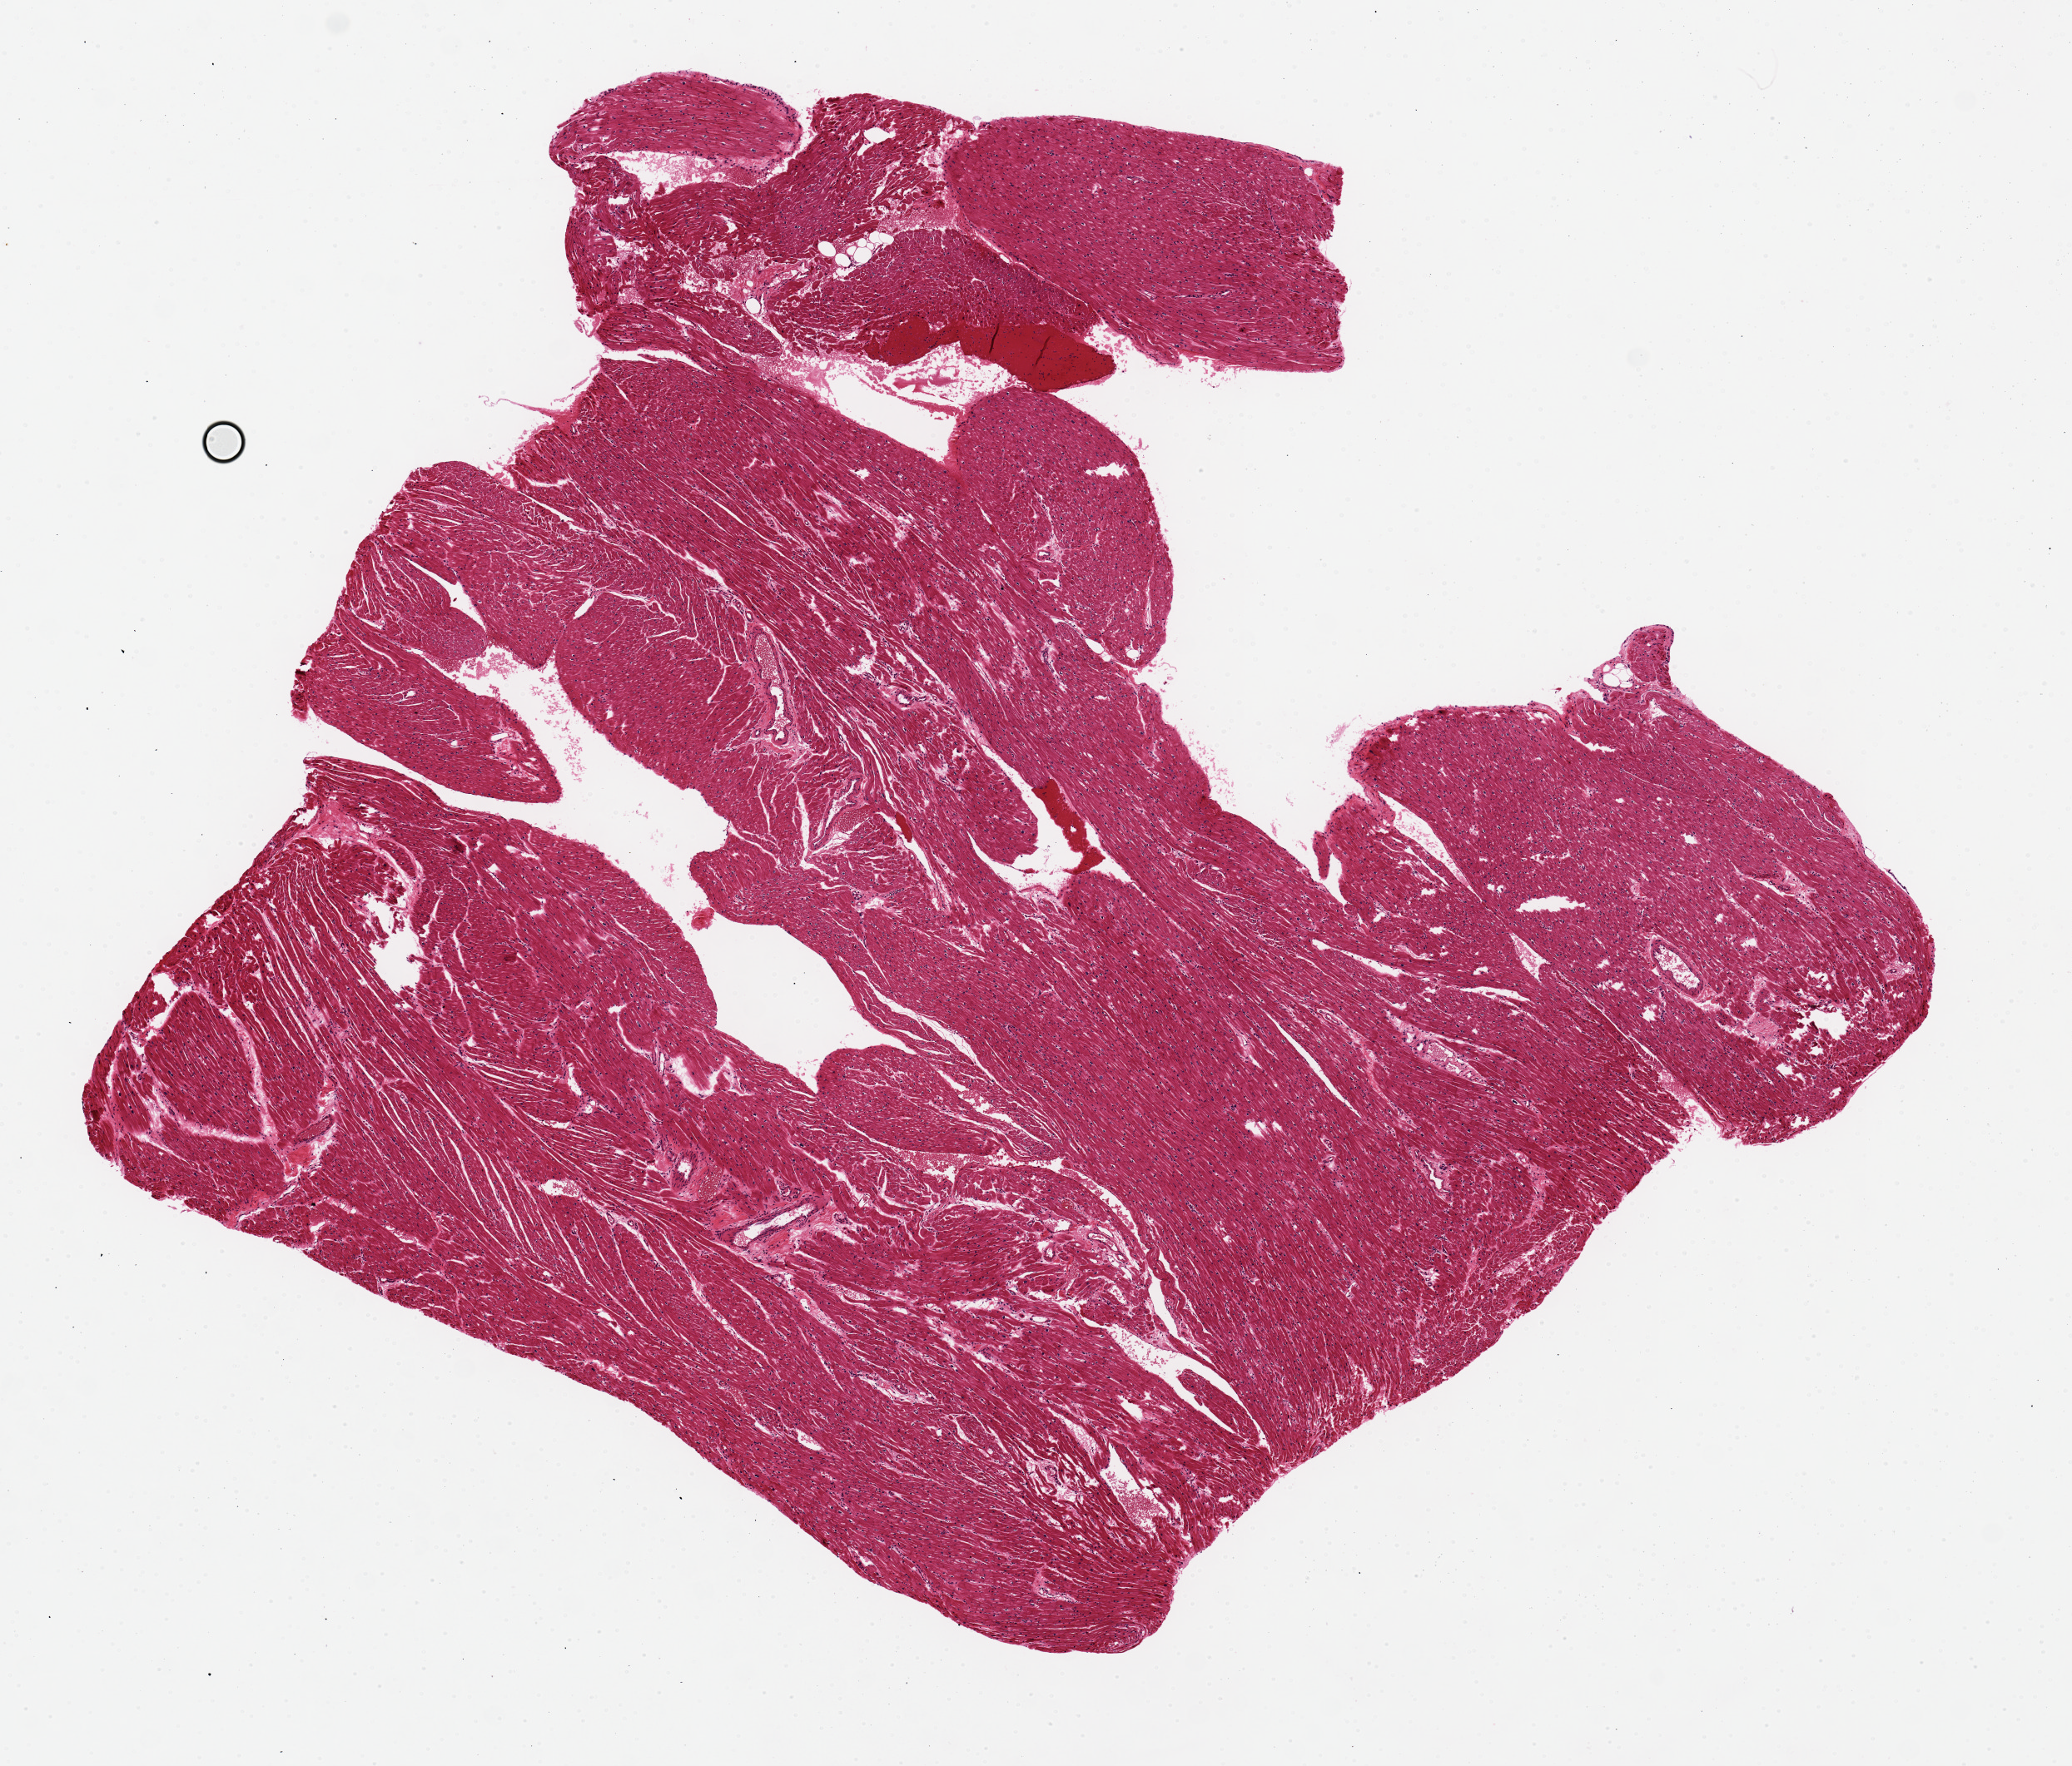
Digitized hematoxylin and eosin (H&E)-stained section, brightfield — low-resolution overview of the scanned area, about 9.8 x 8.4 mm, PAXgene-fixed, paraffin-embedded tissue, section of heart (target tissue), donor tissue sample.
Reviewer comment on this tissue sample: Early ischemic changes. 6.6 x 6.4 mm.